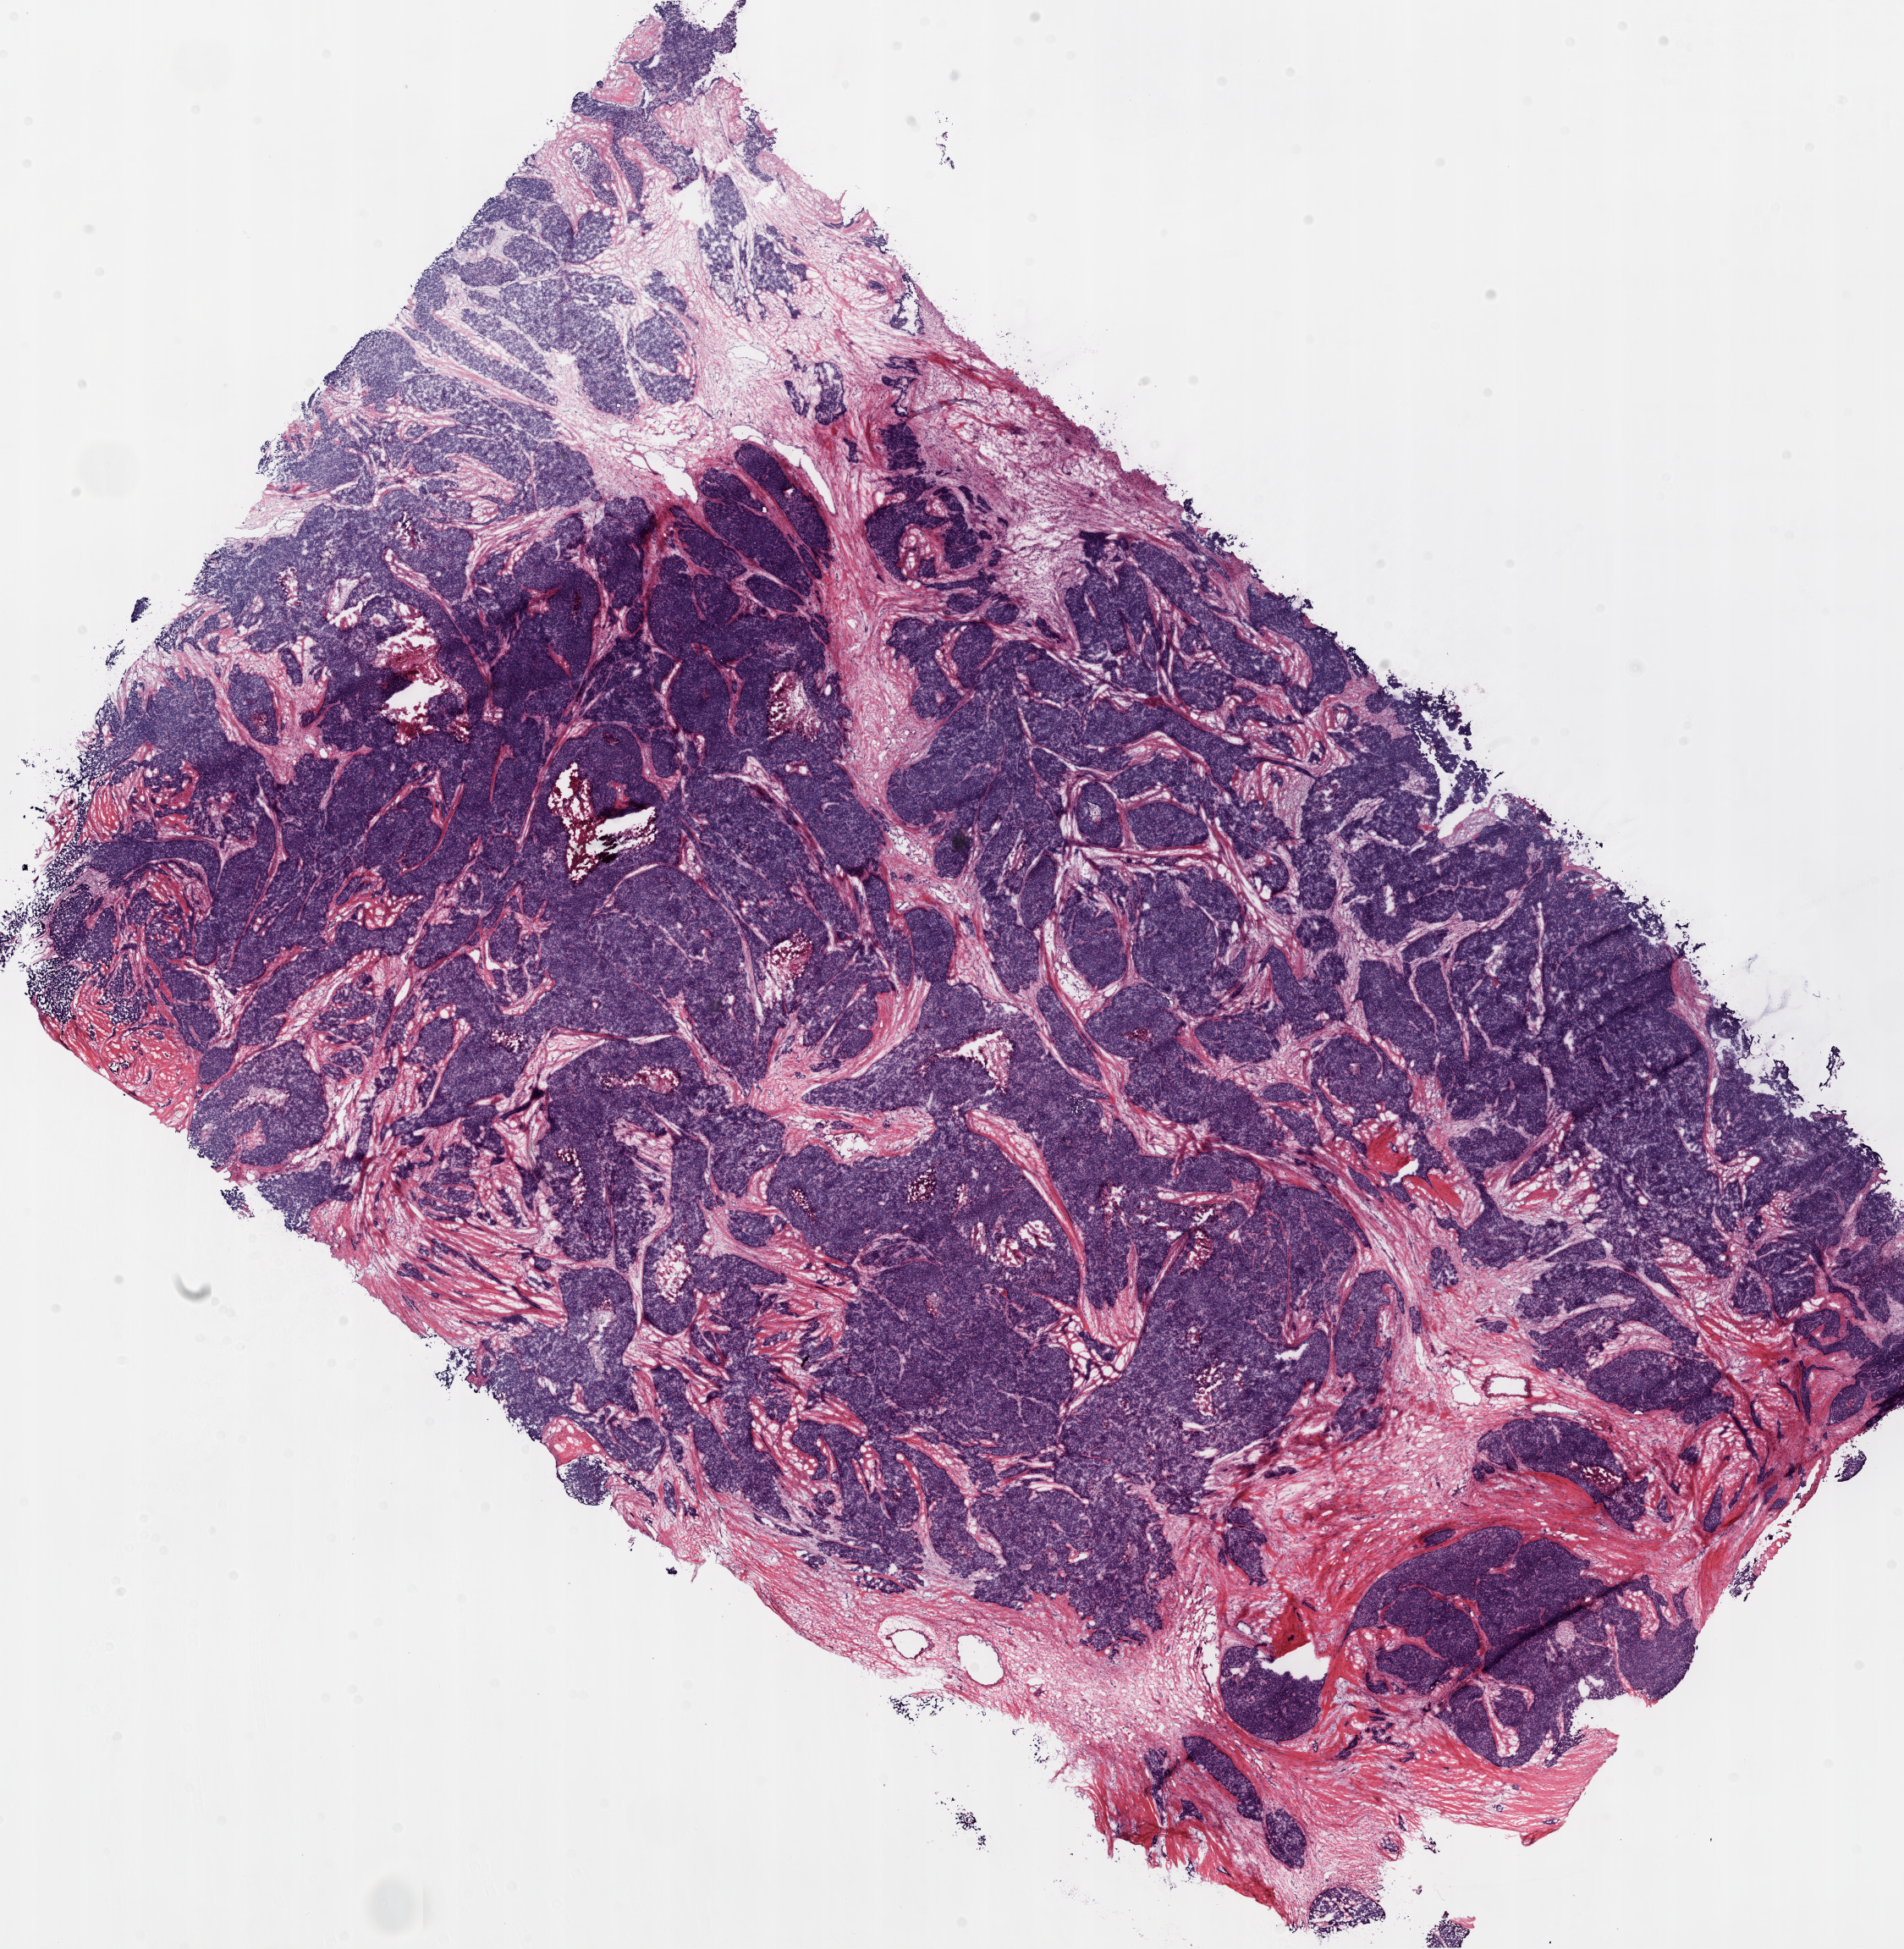
Whole-slide histology image, Hematoxylin and eosin (H&E) stained, shown as a low-resolution overview of the whole scanned area (about 18.1 x 18.5 mm, from a 20x scan), frozen section, ovary, primary tumour sample. Patient: female, age at initial diagnosis 73 years.
Histologic diagnosis: Serous cystadenocarcinoma, NOS.